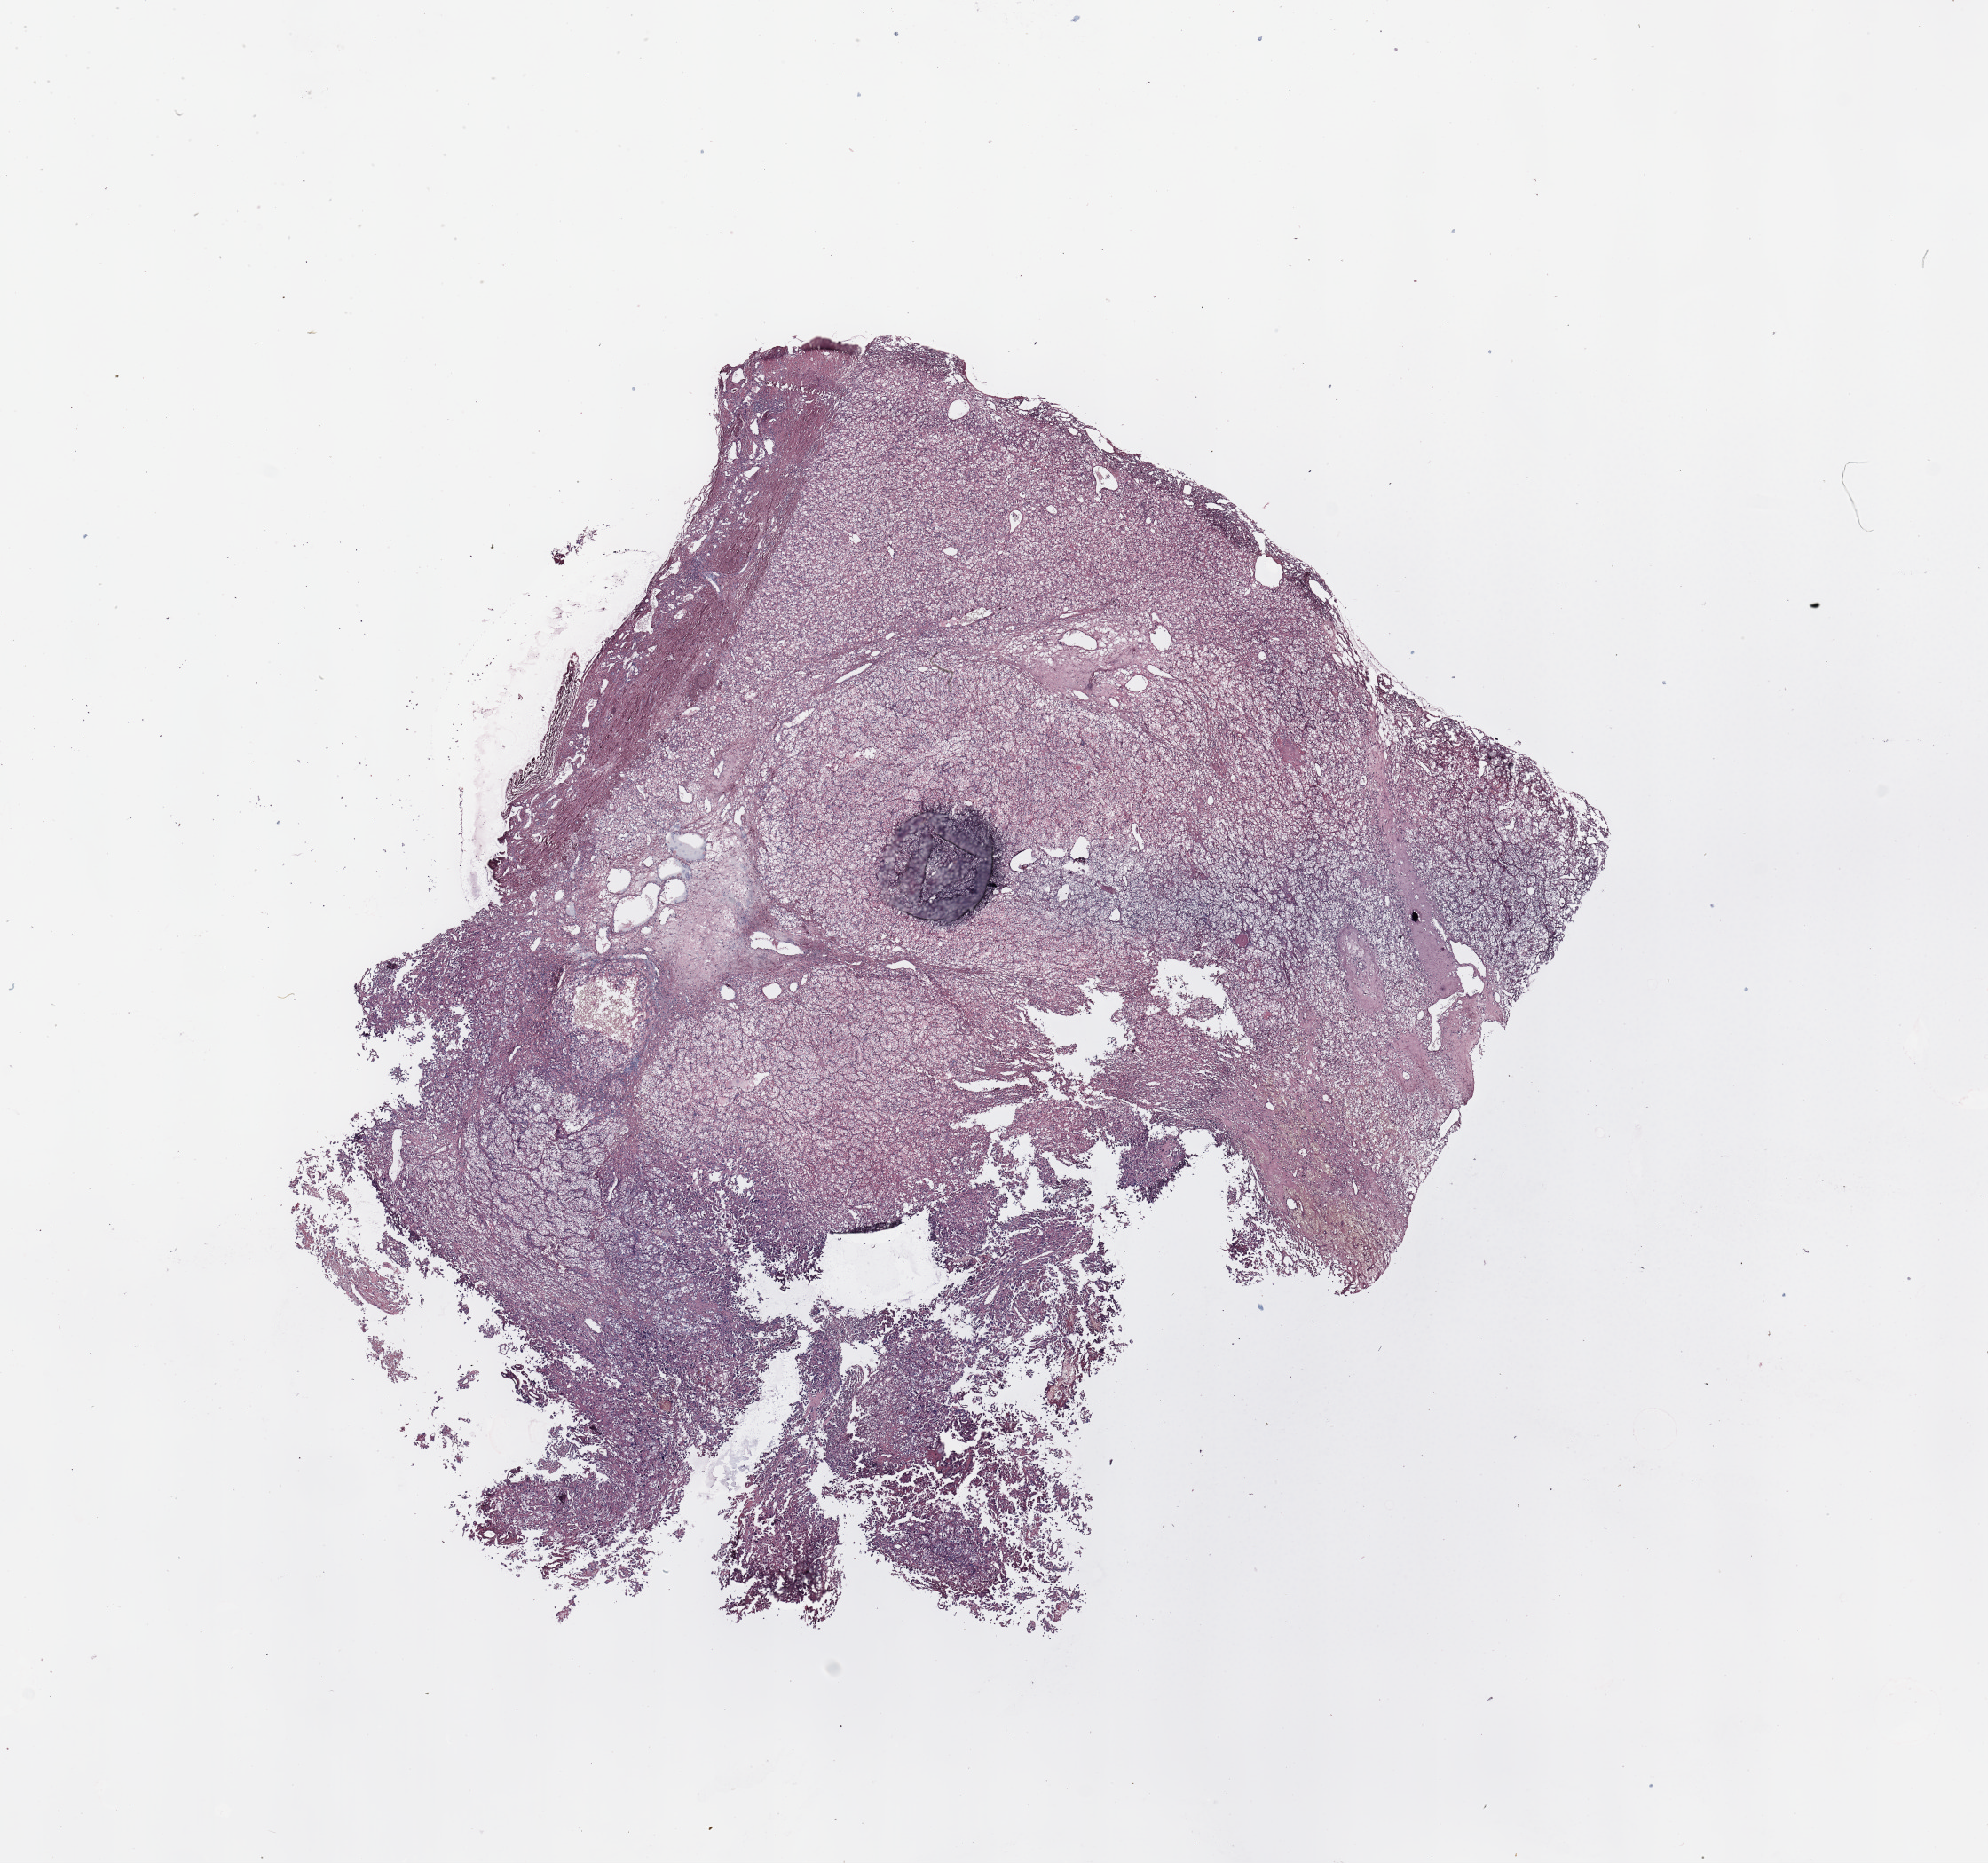
Whole-slide histology image, H&E, a low-resolution overview of the entire scanned area, about 17.7 x 16.6 mm (from a 20x scan), tumour tissue sample, sampled site: kidney. Female, 56 y/o. Slide review estimates, as recorded: tumour nuclei 85%, necrosis 5%.
Histologic diagnosis: Renal cell carcinoma, NOS.